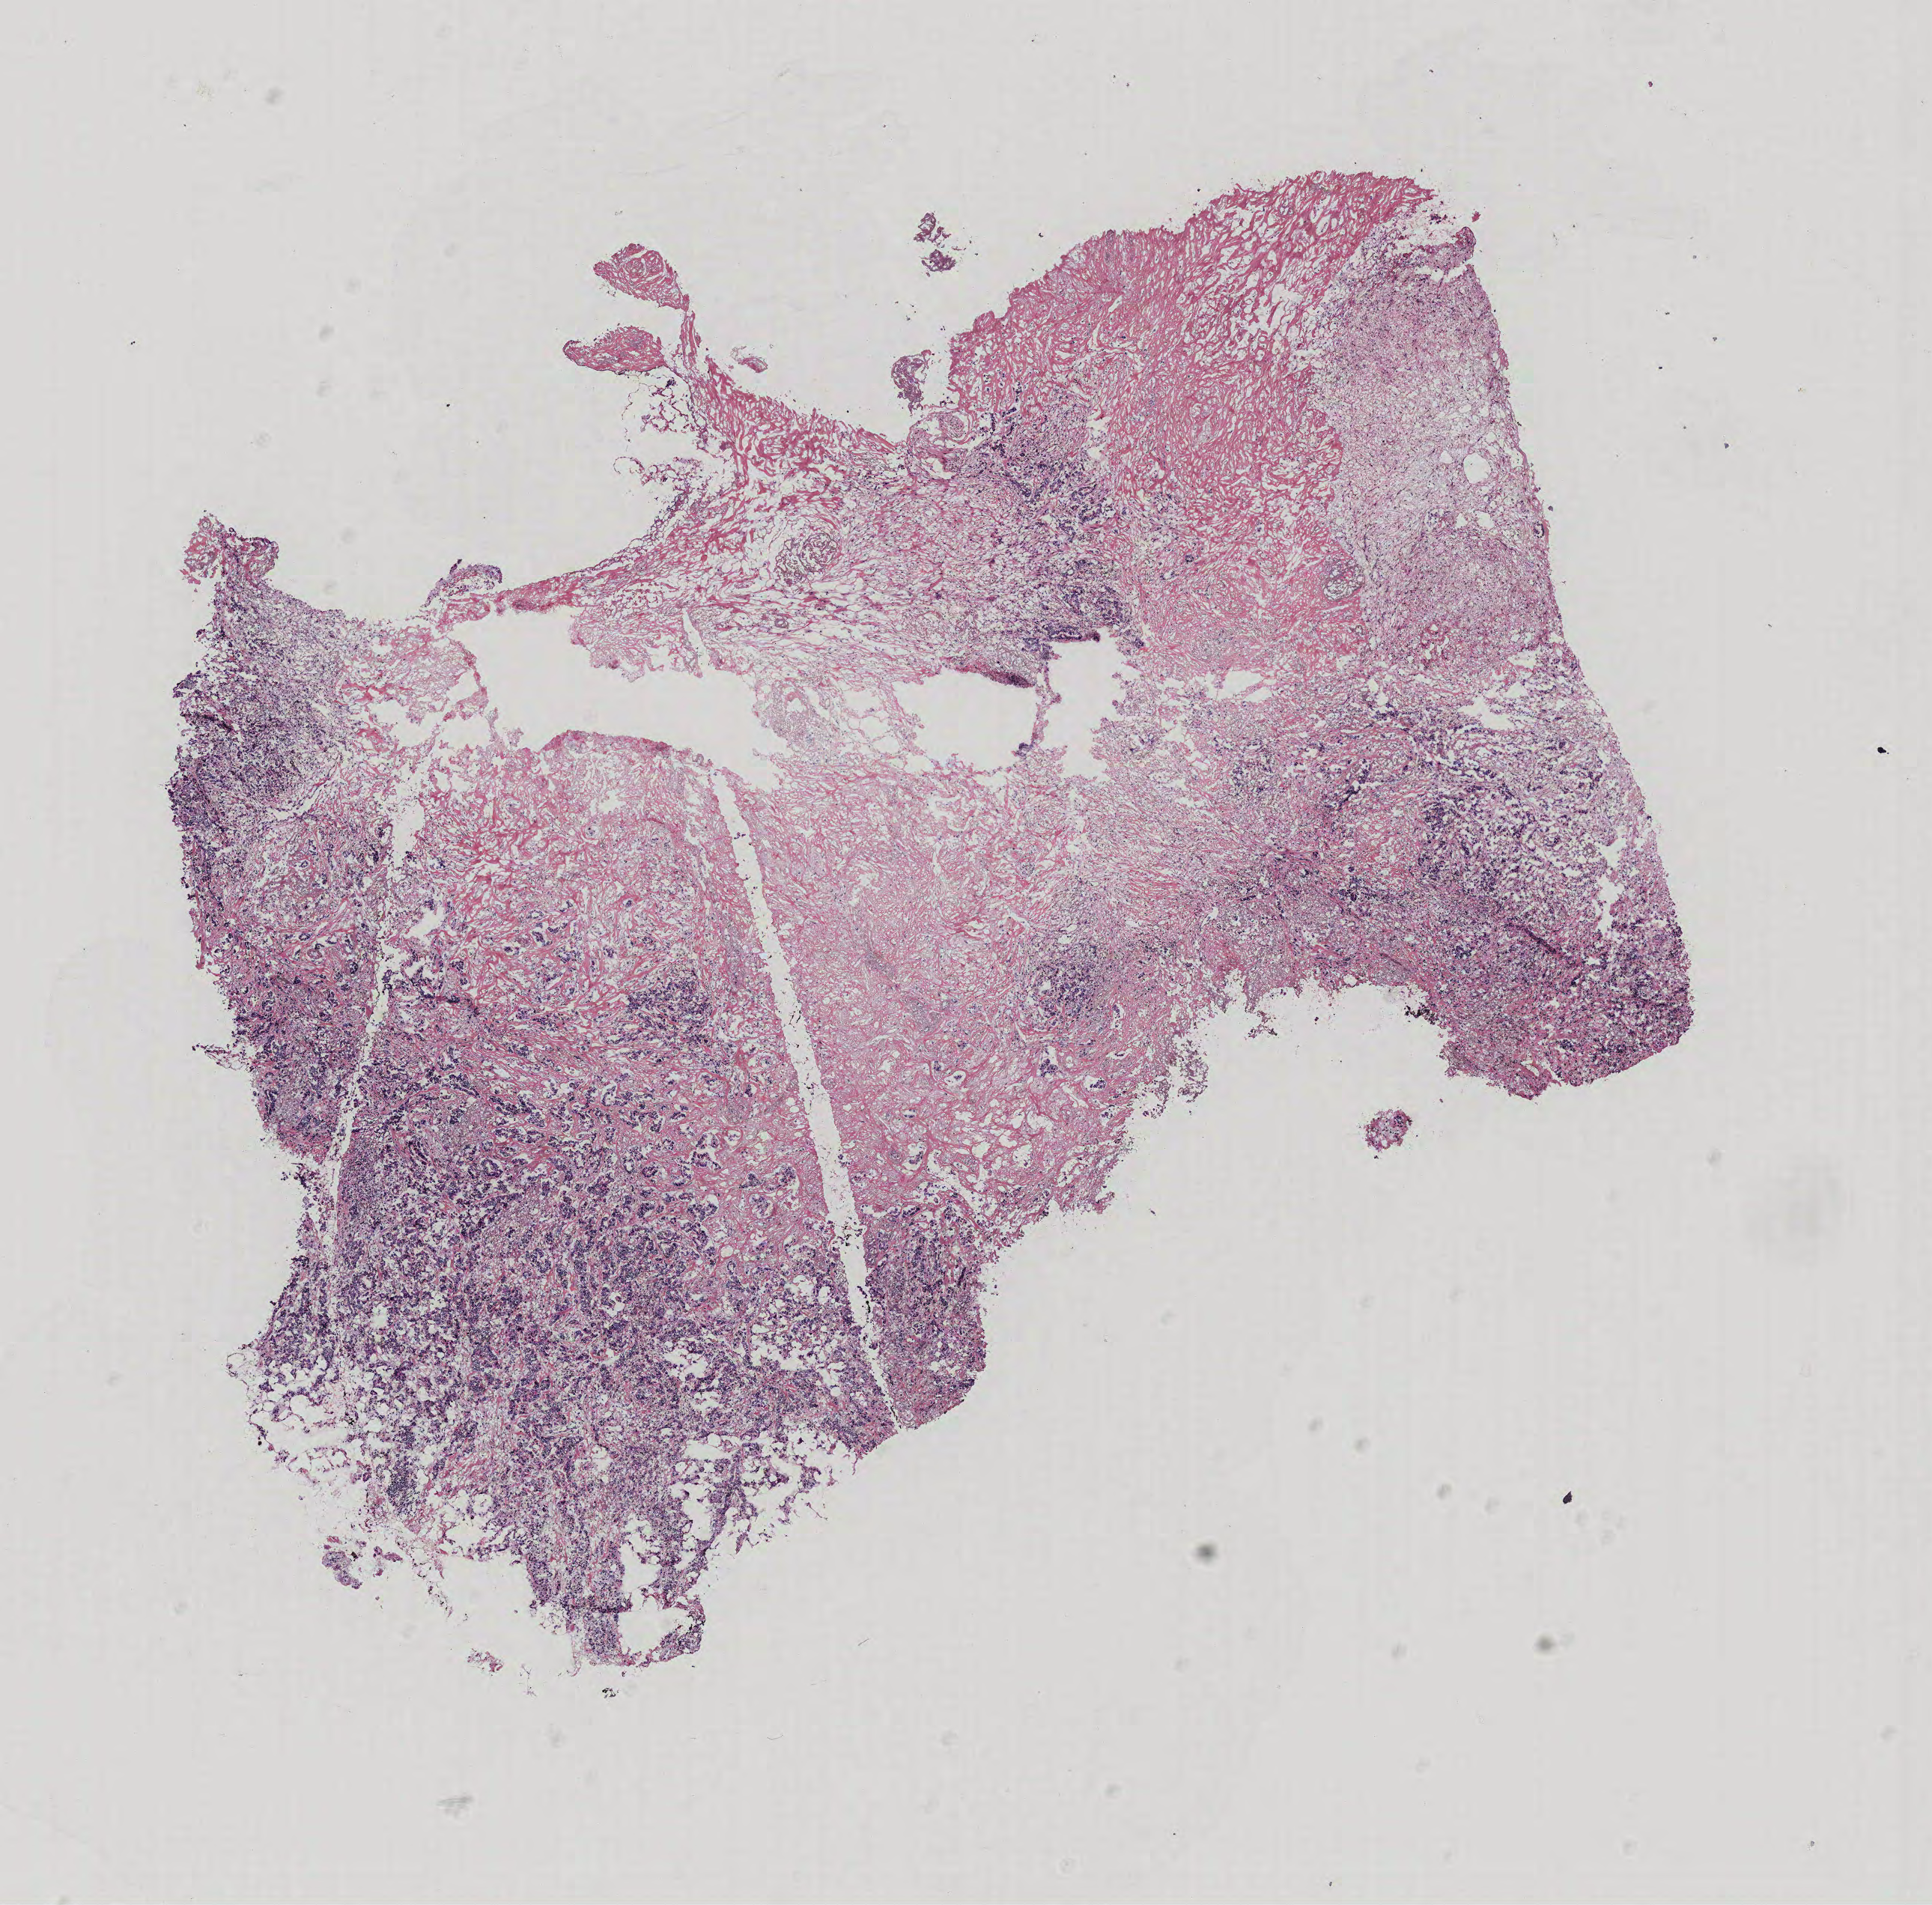
Hematoxylin and eosin (H&E) stained whole-slide image — a low-resolution overview of the entire scanned area, about 10.3 x 10.2 mm (slide scanned at 40x), breast, tissue type not recorded. Female, 77 y/o.
Patient diagnosis: Infiltrating duct carcinoma, NOS.